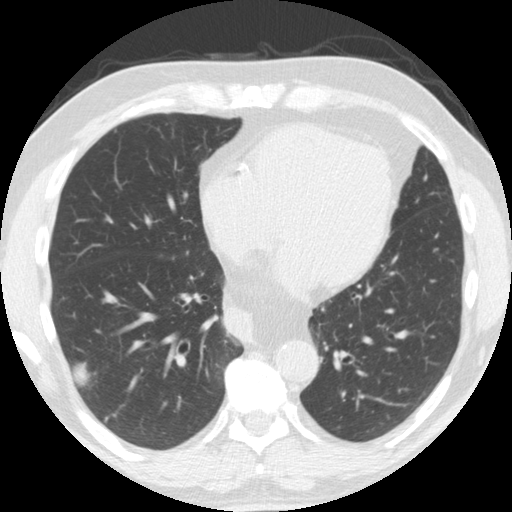
Low-dose screening chest CT, one axial slice; slice 68 of 174 in the series (ordered by position); reconstruction kernel STANDARD; lung window (W 1500 / L -600 HU); 2.5 mm slice thickness; 512 × 512 image matrix, field of view 341 × 341 mm.
Annotated regions visible in this slice (outlined manually by an expert reader):
- lesion 1 (tumor, lower lobe of right lung): bounding box [x1, y1, x2, y2] px = [75, 363, 90, 386]